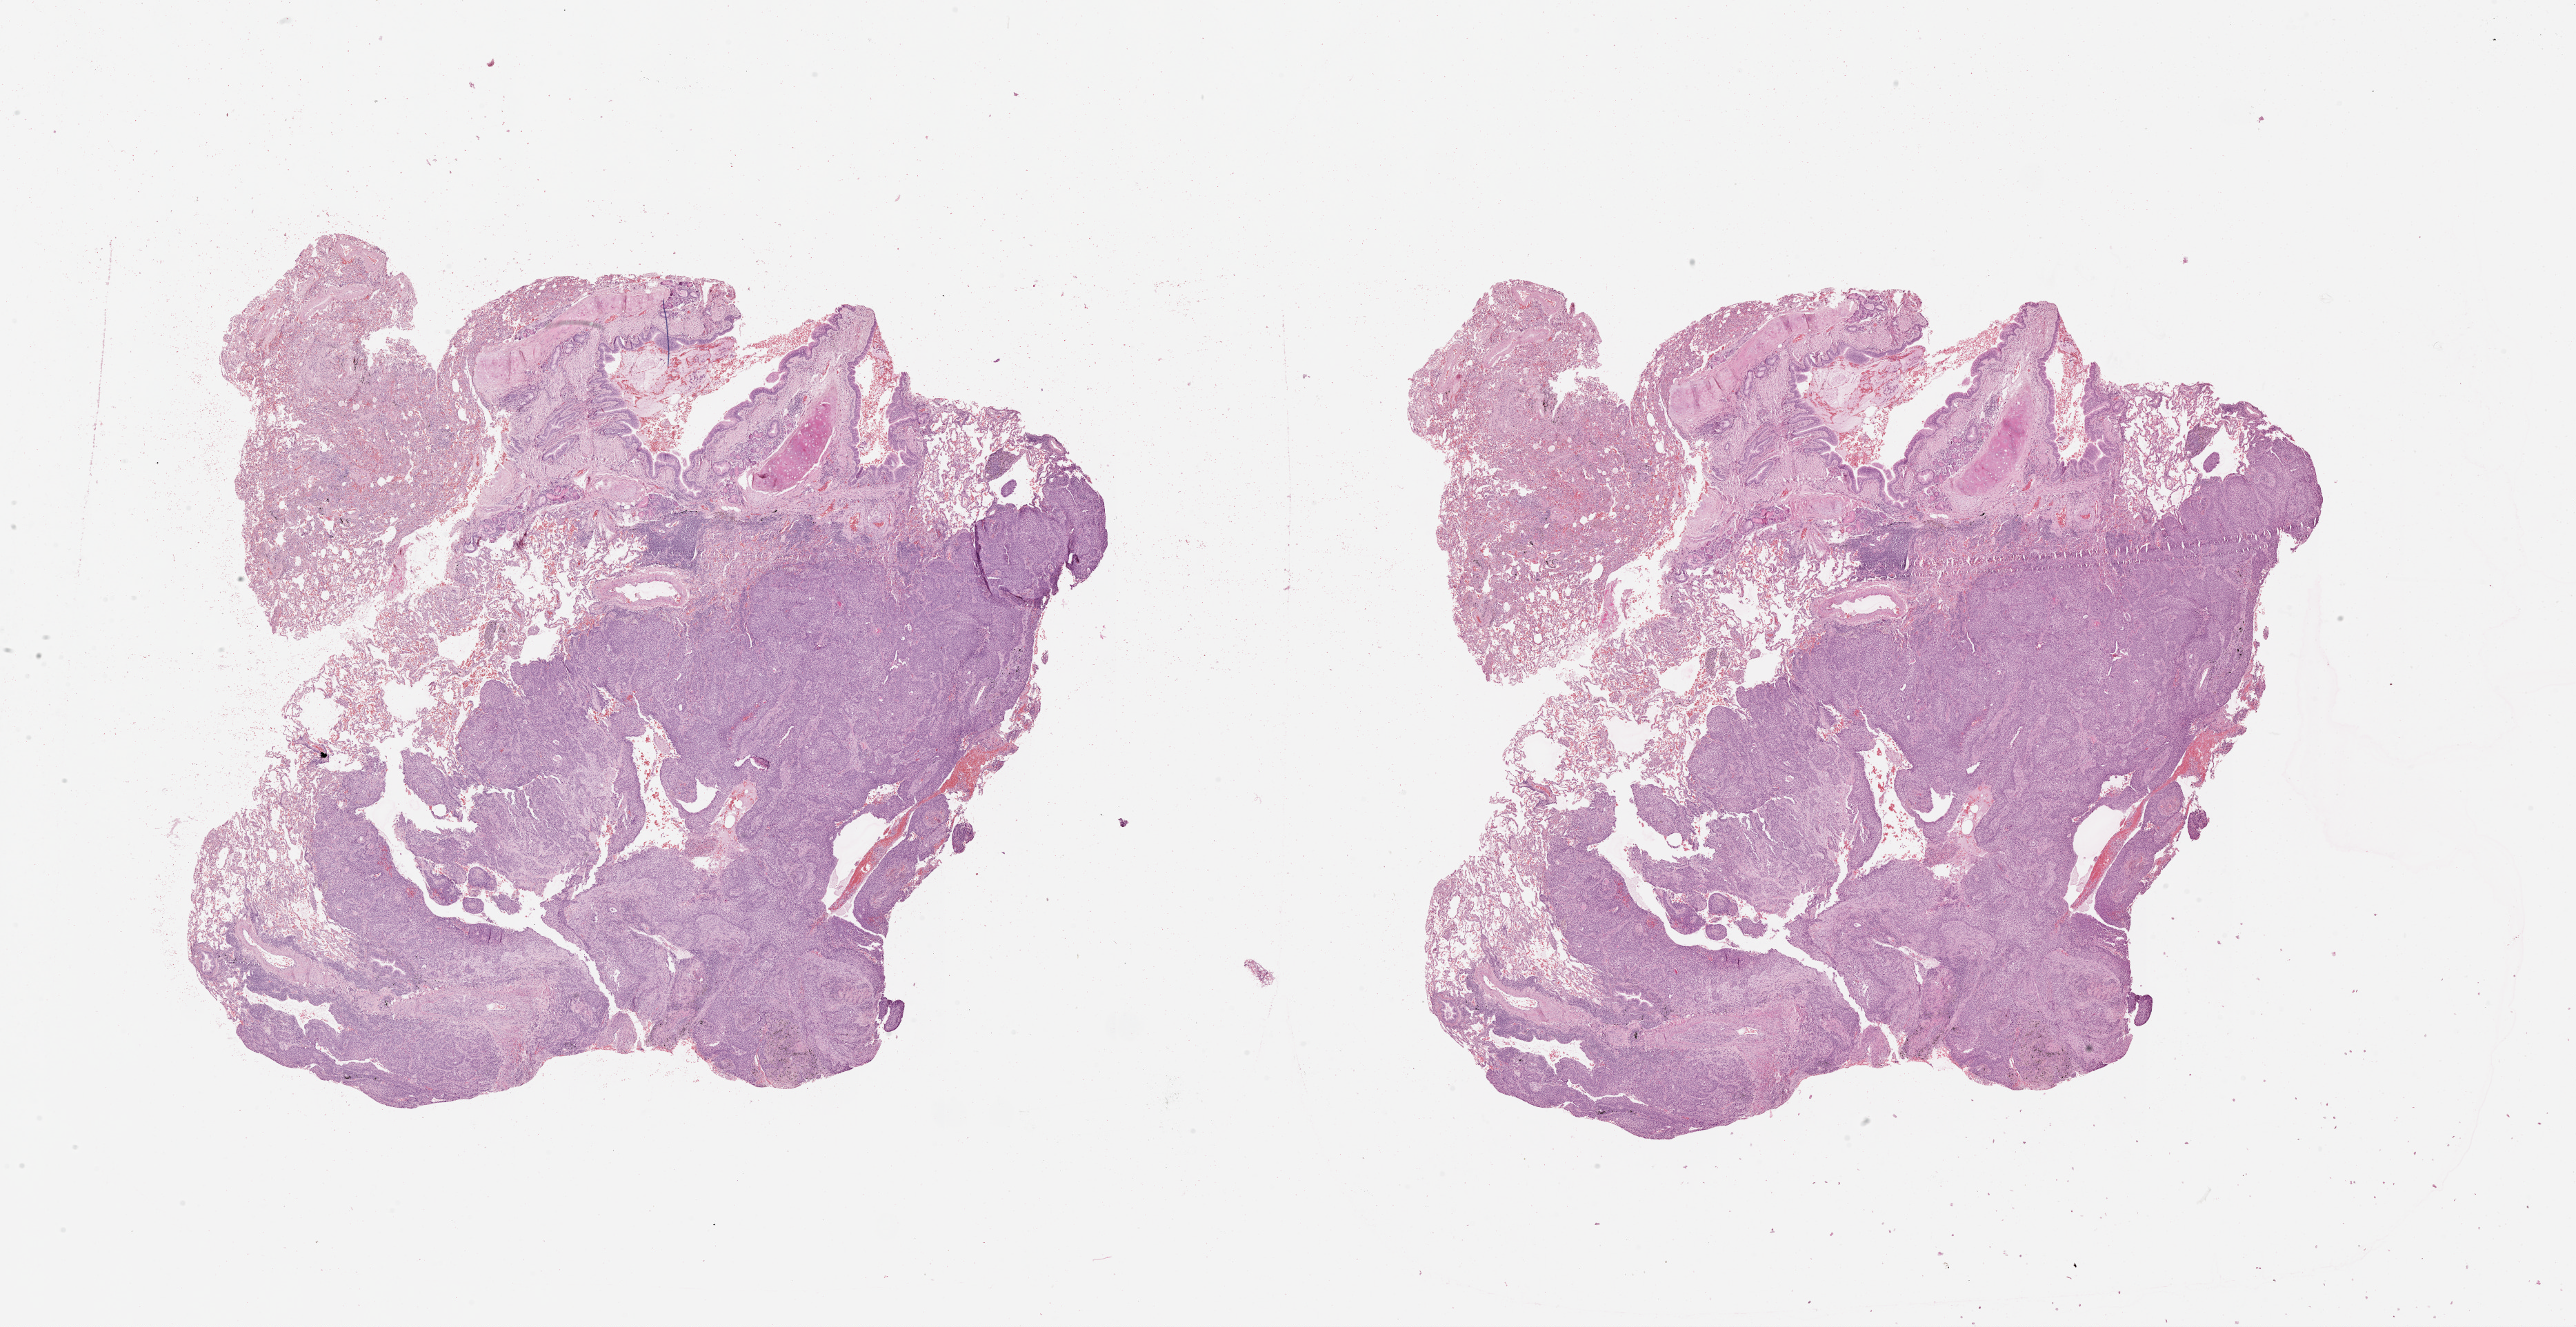
H&E-stained whole-slide image — whole scanned area (about 30.1 x 15.5 mm, from a 20x scan) shown as a low-resolution overview; lung, tumour tissue. 69-year-old male patient.
- patient diagnosis (cohort enrolment): squamous cell carcinoma (lung)